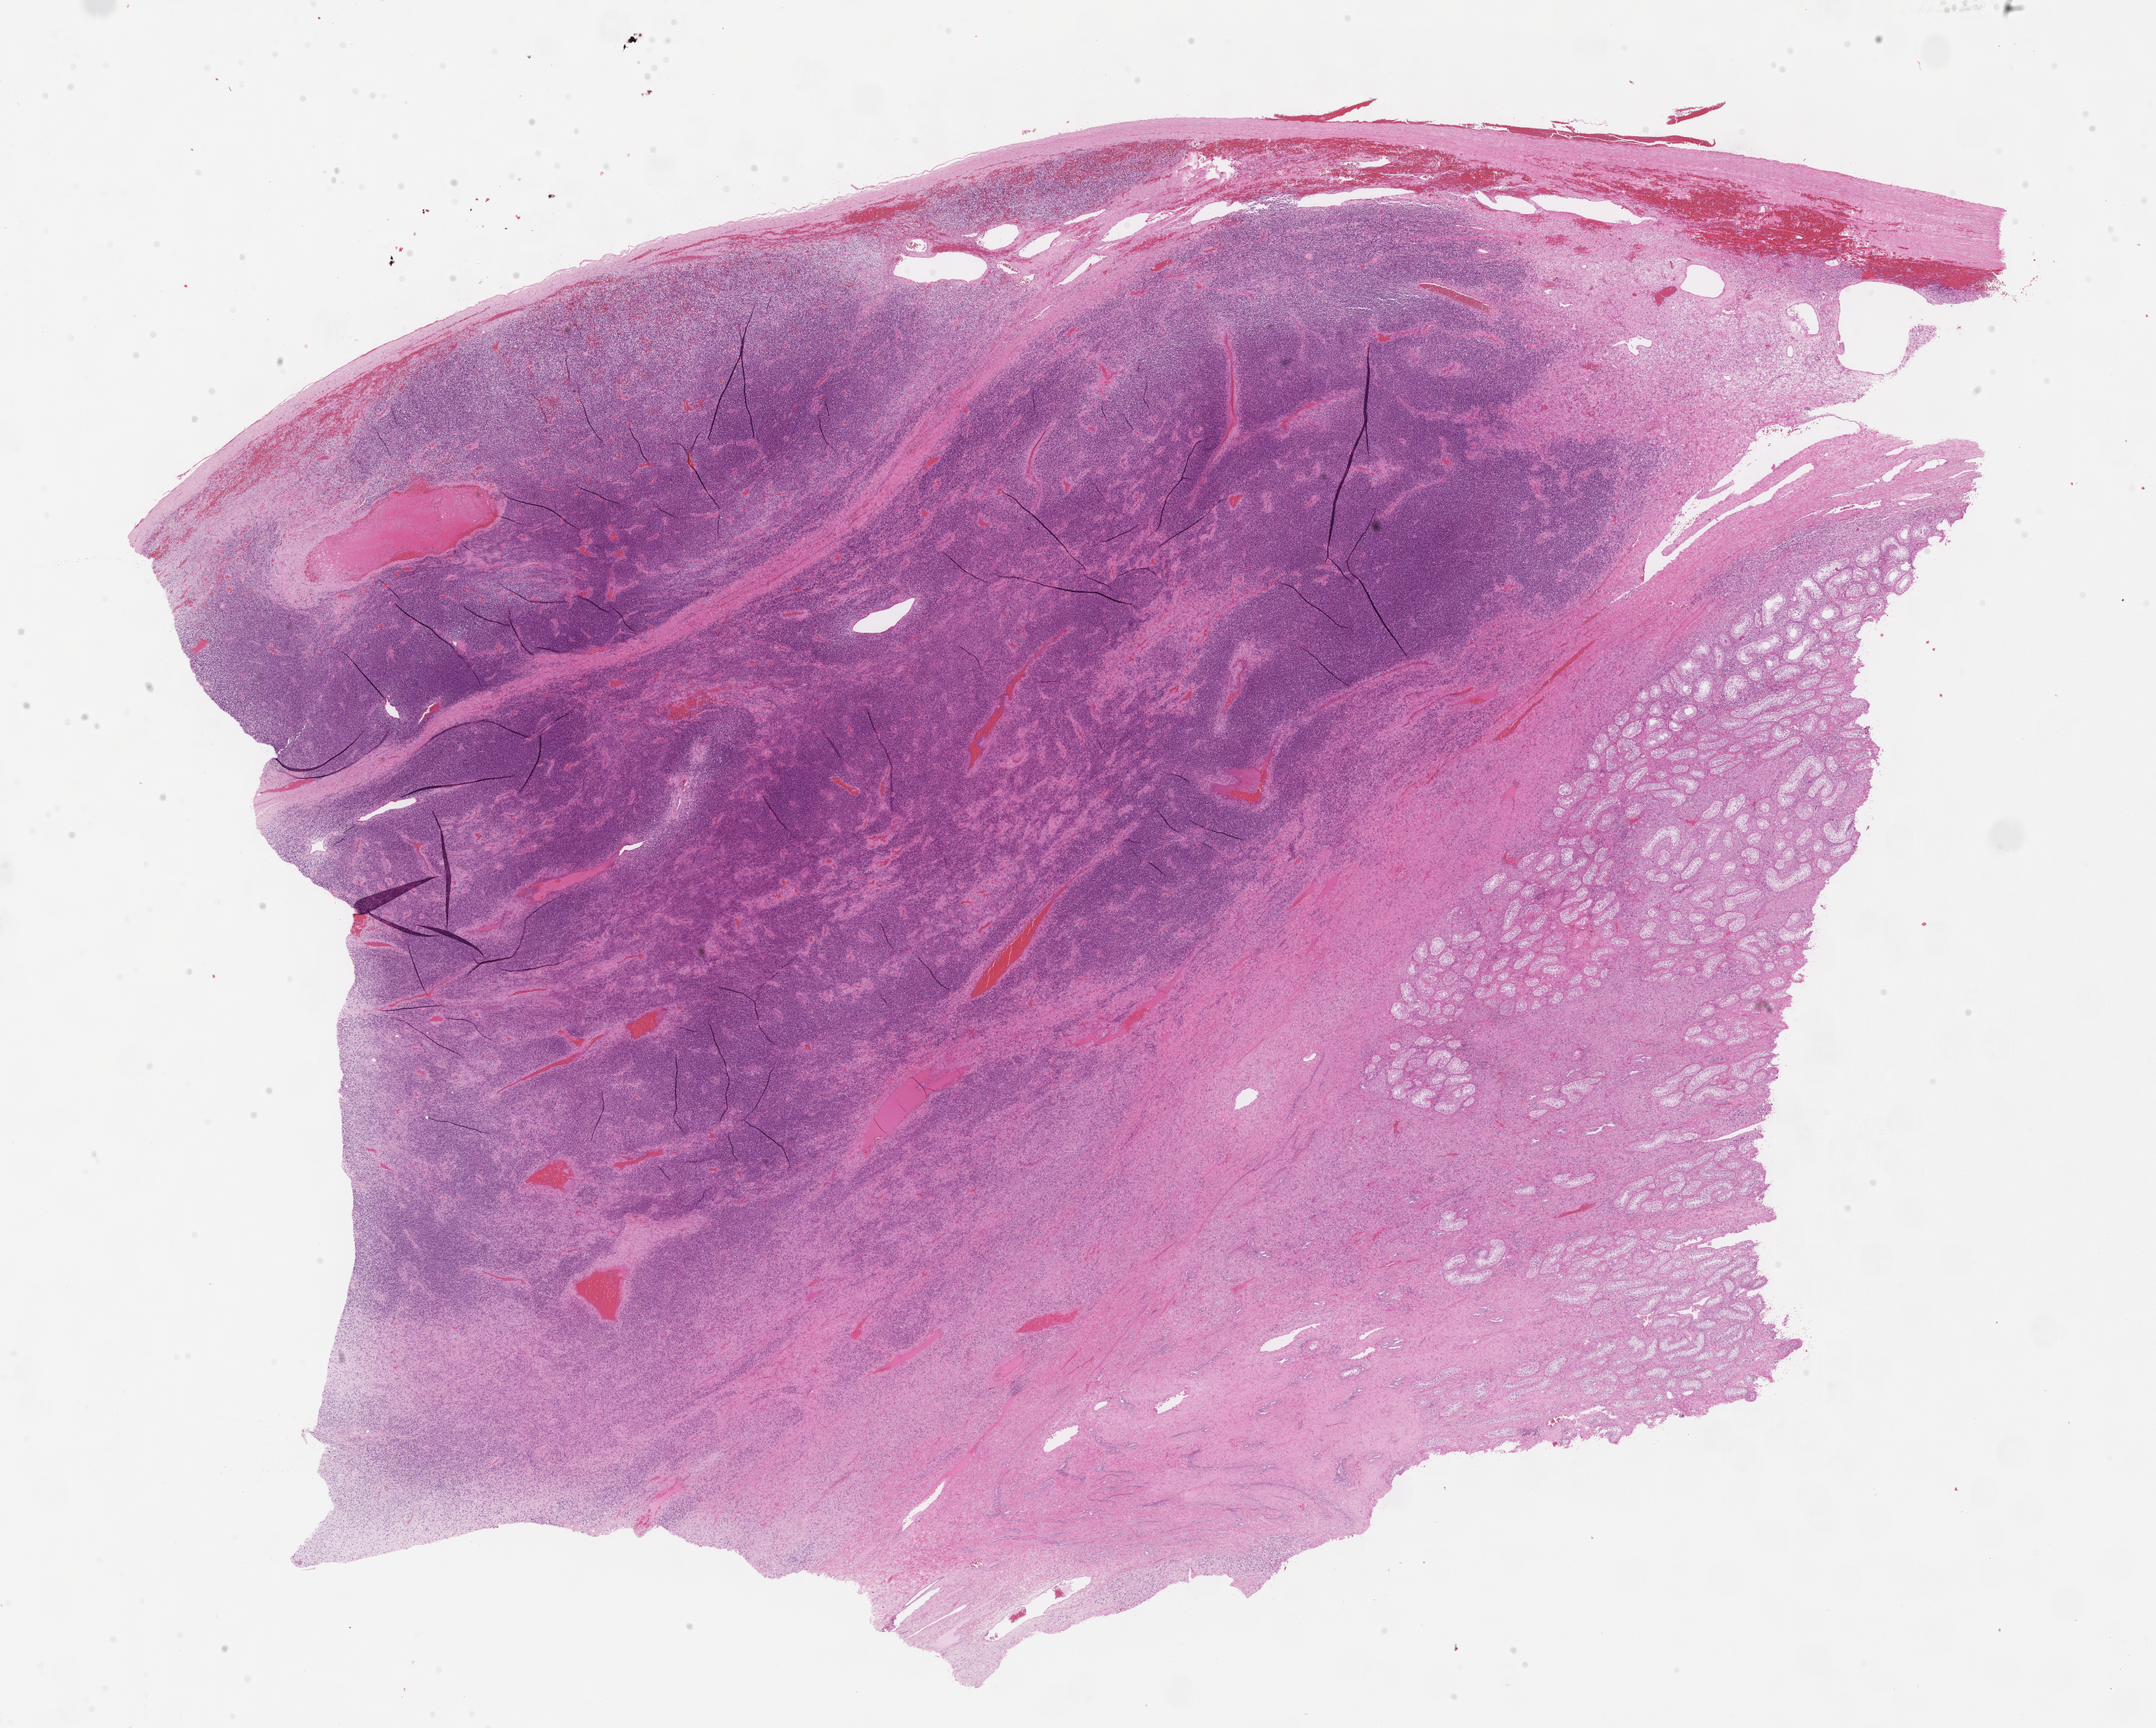
Hematoxylin and eosin (H&E) whole-slide image of tumor tissue, whole scanned area (about 22.6 x 18.1 mm) shown as a low-resolution overview. FFPE section. Sample anatomic site: testicle, left. Male patient, age at diagnosis 14.4 years.
• stage (as recorded): 4
• metastatic status at presentation (as recorded): metastatic
• diagnosis: rhabdomyosarcoma; histological classification: embryonal rhabdomyosarcoma